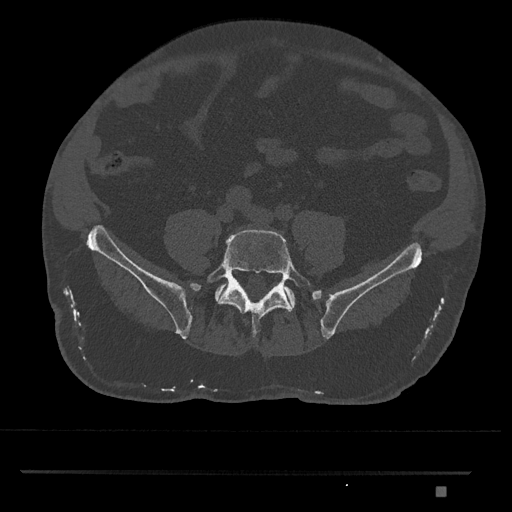
CT including the spine, one axial slice; slice 552 of 1134 in the series (ordered by position); reconstruction kernel Br40s/3; bone window (W 1800 / L 400 HU); 0.5 mm slice thickness; 512 × 512 image matrix. Male patient, age 65 years. Case-level facts recorded for this patient, not image findings: primary cancer: prostate.
Outlined on this slice (semi-automatic segmentation, software-assisted and operator-edited):
- L5 vertebra: bounding box <207,229,313,338> (left, top, right, bottom; pixels)